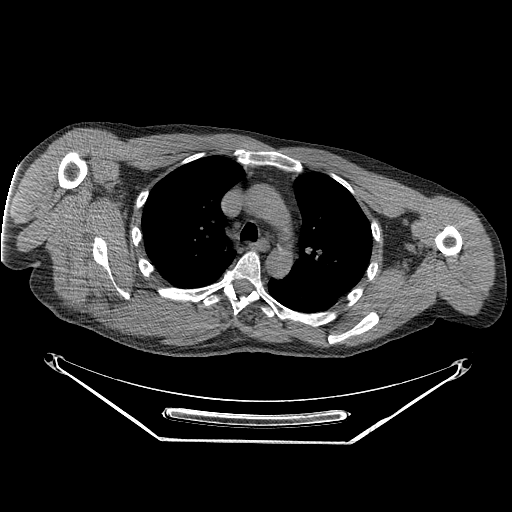
CT of an extremity soft-tissue mass (from a PET/CT study), one axial slice. Position 185 of 267 along the scan axis. 140 kVp. Soft-tissue window (W 400 / L 40 HU). 512 × 512 image matrix. Male patient. From the clinical record (not read from this slice): histological type: pleiomorphic spindle cell undifferentiated; grade: high; site of the primary tumour: right parascapusular.
Outlined on this slice (expert contour drawn on MRI and transferred to this co-registered scan by the dataset authors):
- gross tumour volume including surrounding oedema: bounding box [x1, y1, x2, y2] px = [82, 278, 218, 337]
- gross tumour volume (mass): [89, 281, 184, 332]